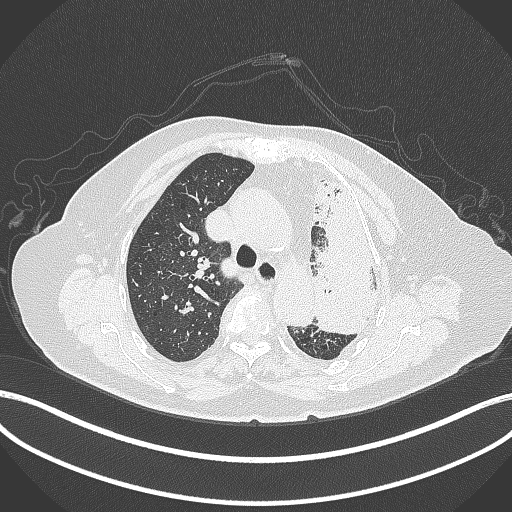
Chest CT, one axial slice; position 284 of 399 along the scan axis; lung window (W 1500 / L -600 HU); 1 mm slice thickness; 512 × 512 image matrix, field of view 400 × 400 mm. Patient: female, 75 years. From the clinical record (not read from this slice): clinical TNM (as recorded): T3 N3 M1.
Outlined on this slice (rectangle marked by the reading radiologist):
- lung tumour (recorded histology: adenocarcinoma): bounding box <297,159,392,344> (left, top, right, bottom; pixels)